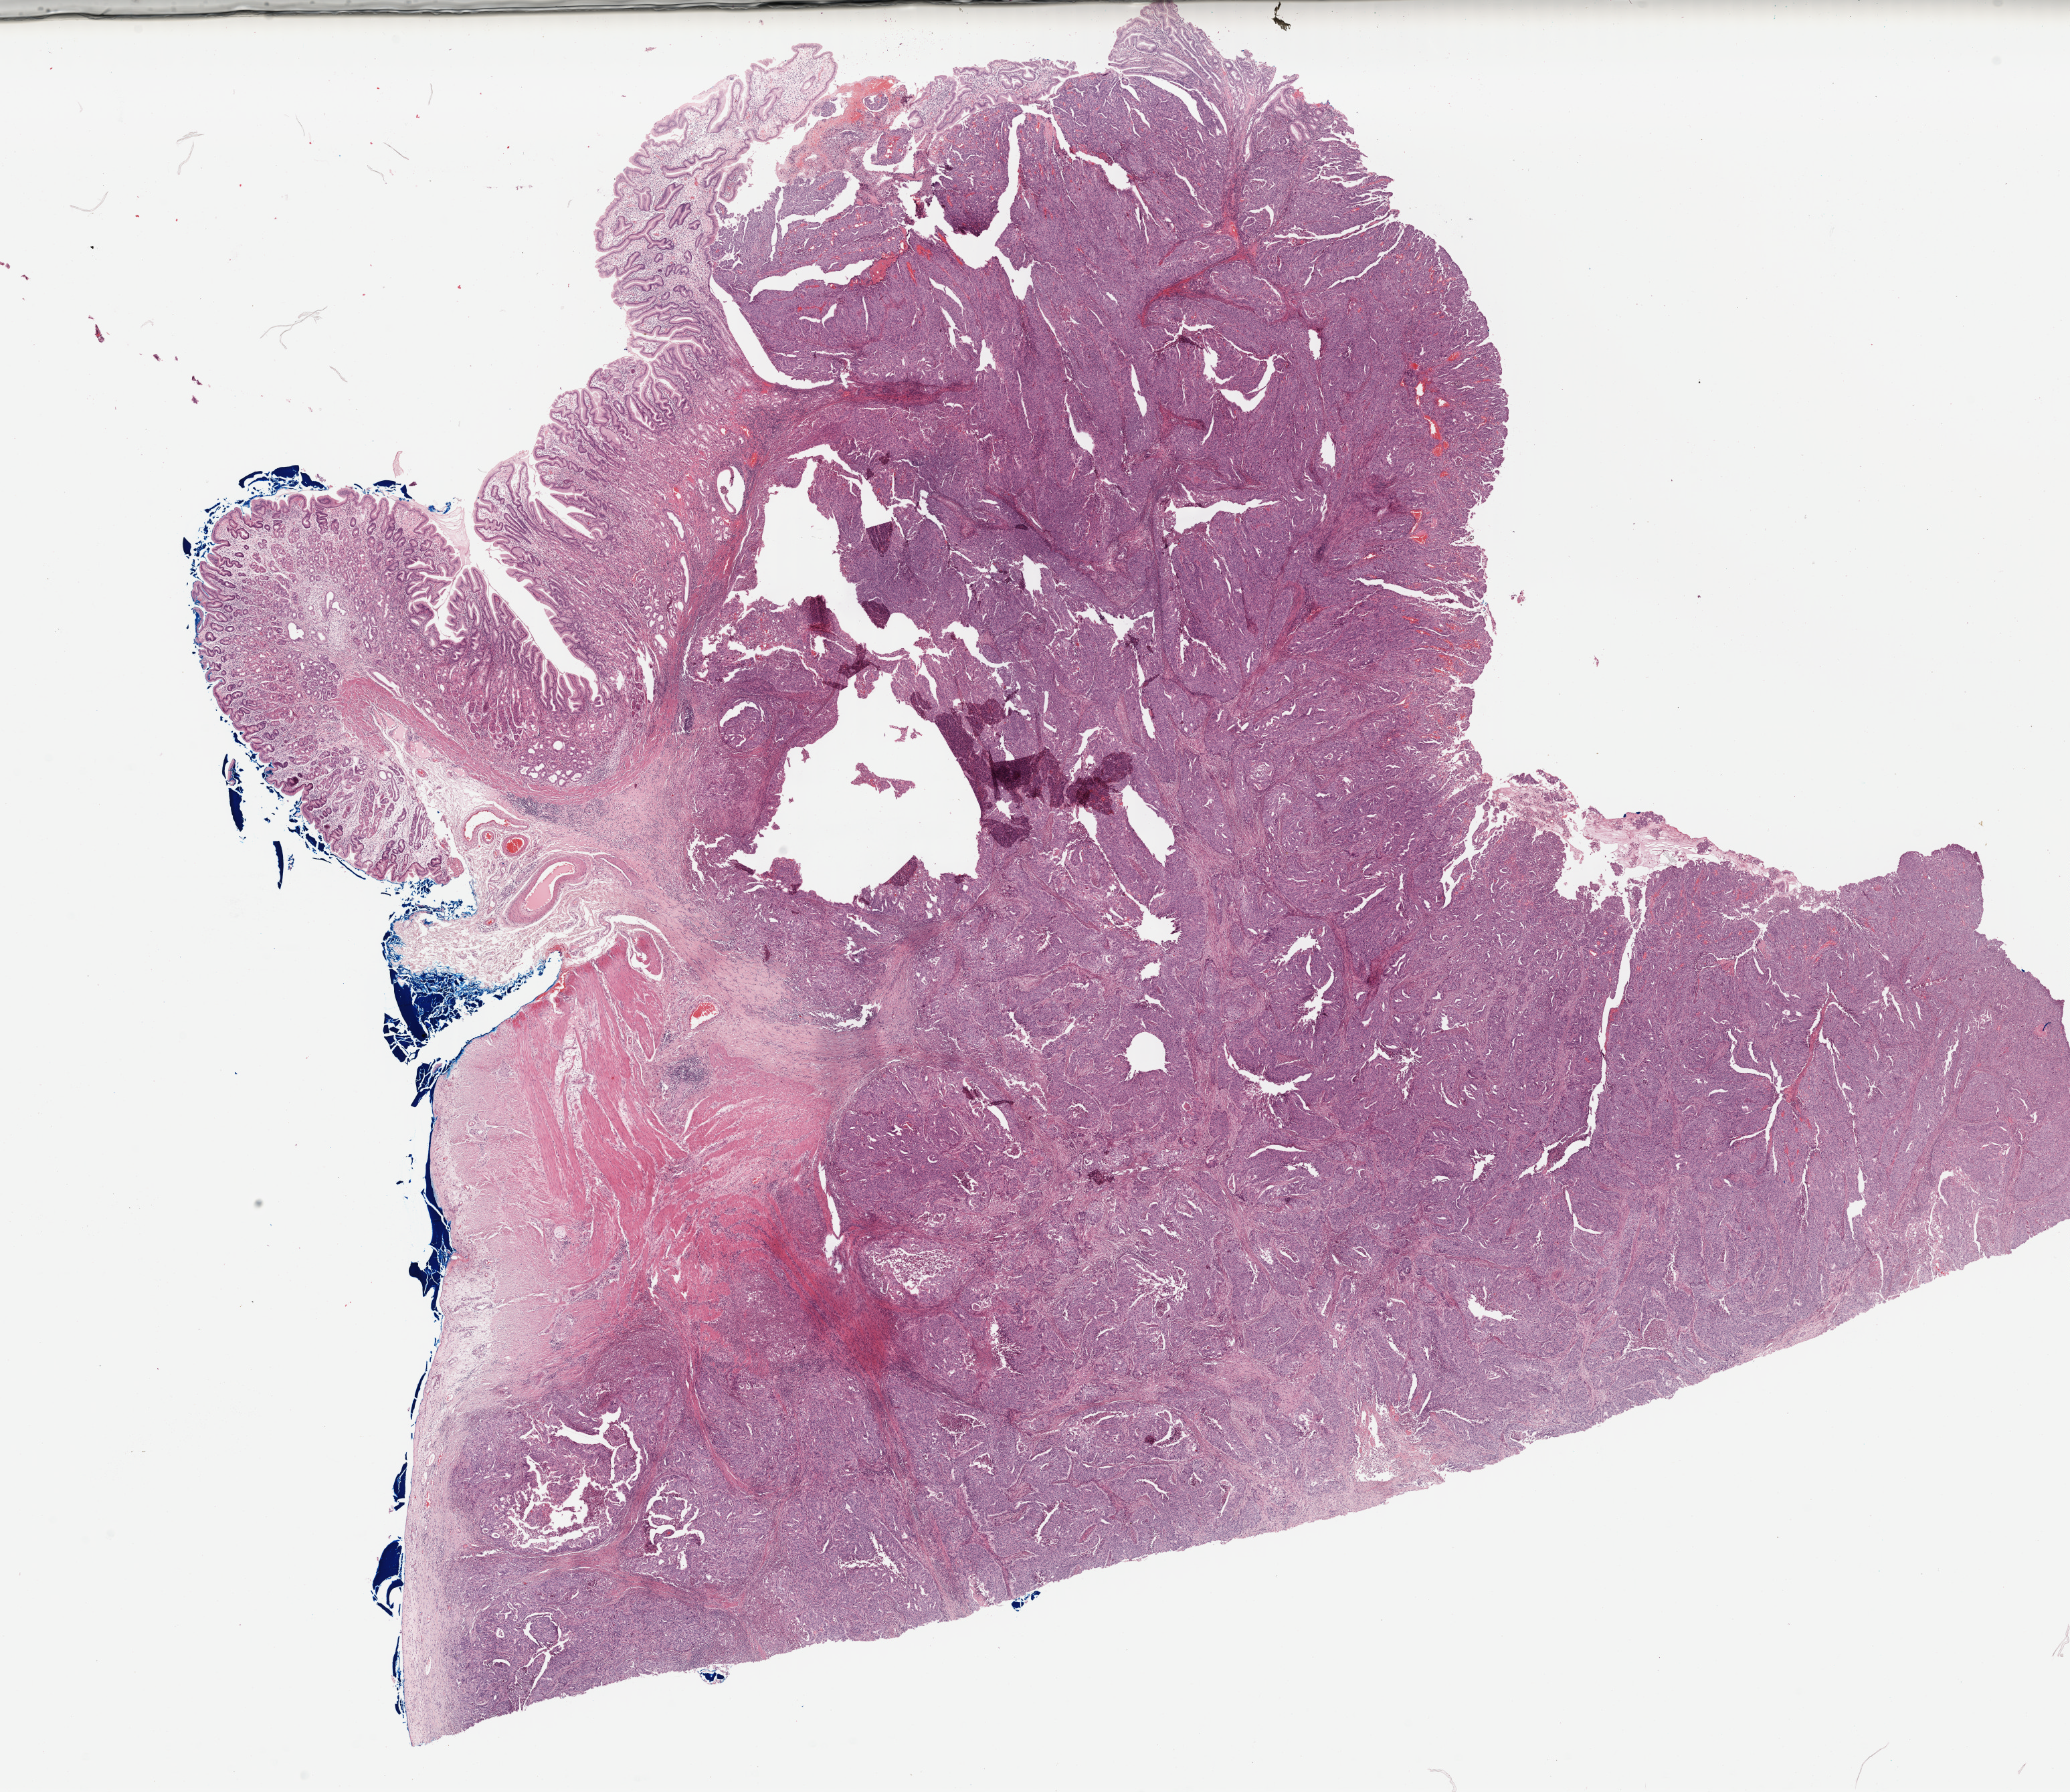
Whole-slide histology image, H&E, whole scanned area (about 24.4 x 21.1 mm) shown as a low-resolution overview, formalin-fixed paraffin-embedded (FFPE) diagnostic section, stomach, primary tumour sample. Patient: male, age at initial diagnosis 57 years. Histologic grade: G3 (poorly differentiated).
* pathologic diagnosis: Tubular adenocarcinoma (fundus of stomach)
* lymph nodes positive (case pathology): 0 of 20 examined
* AJCC pathologic stage: IIA